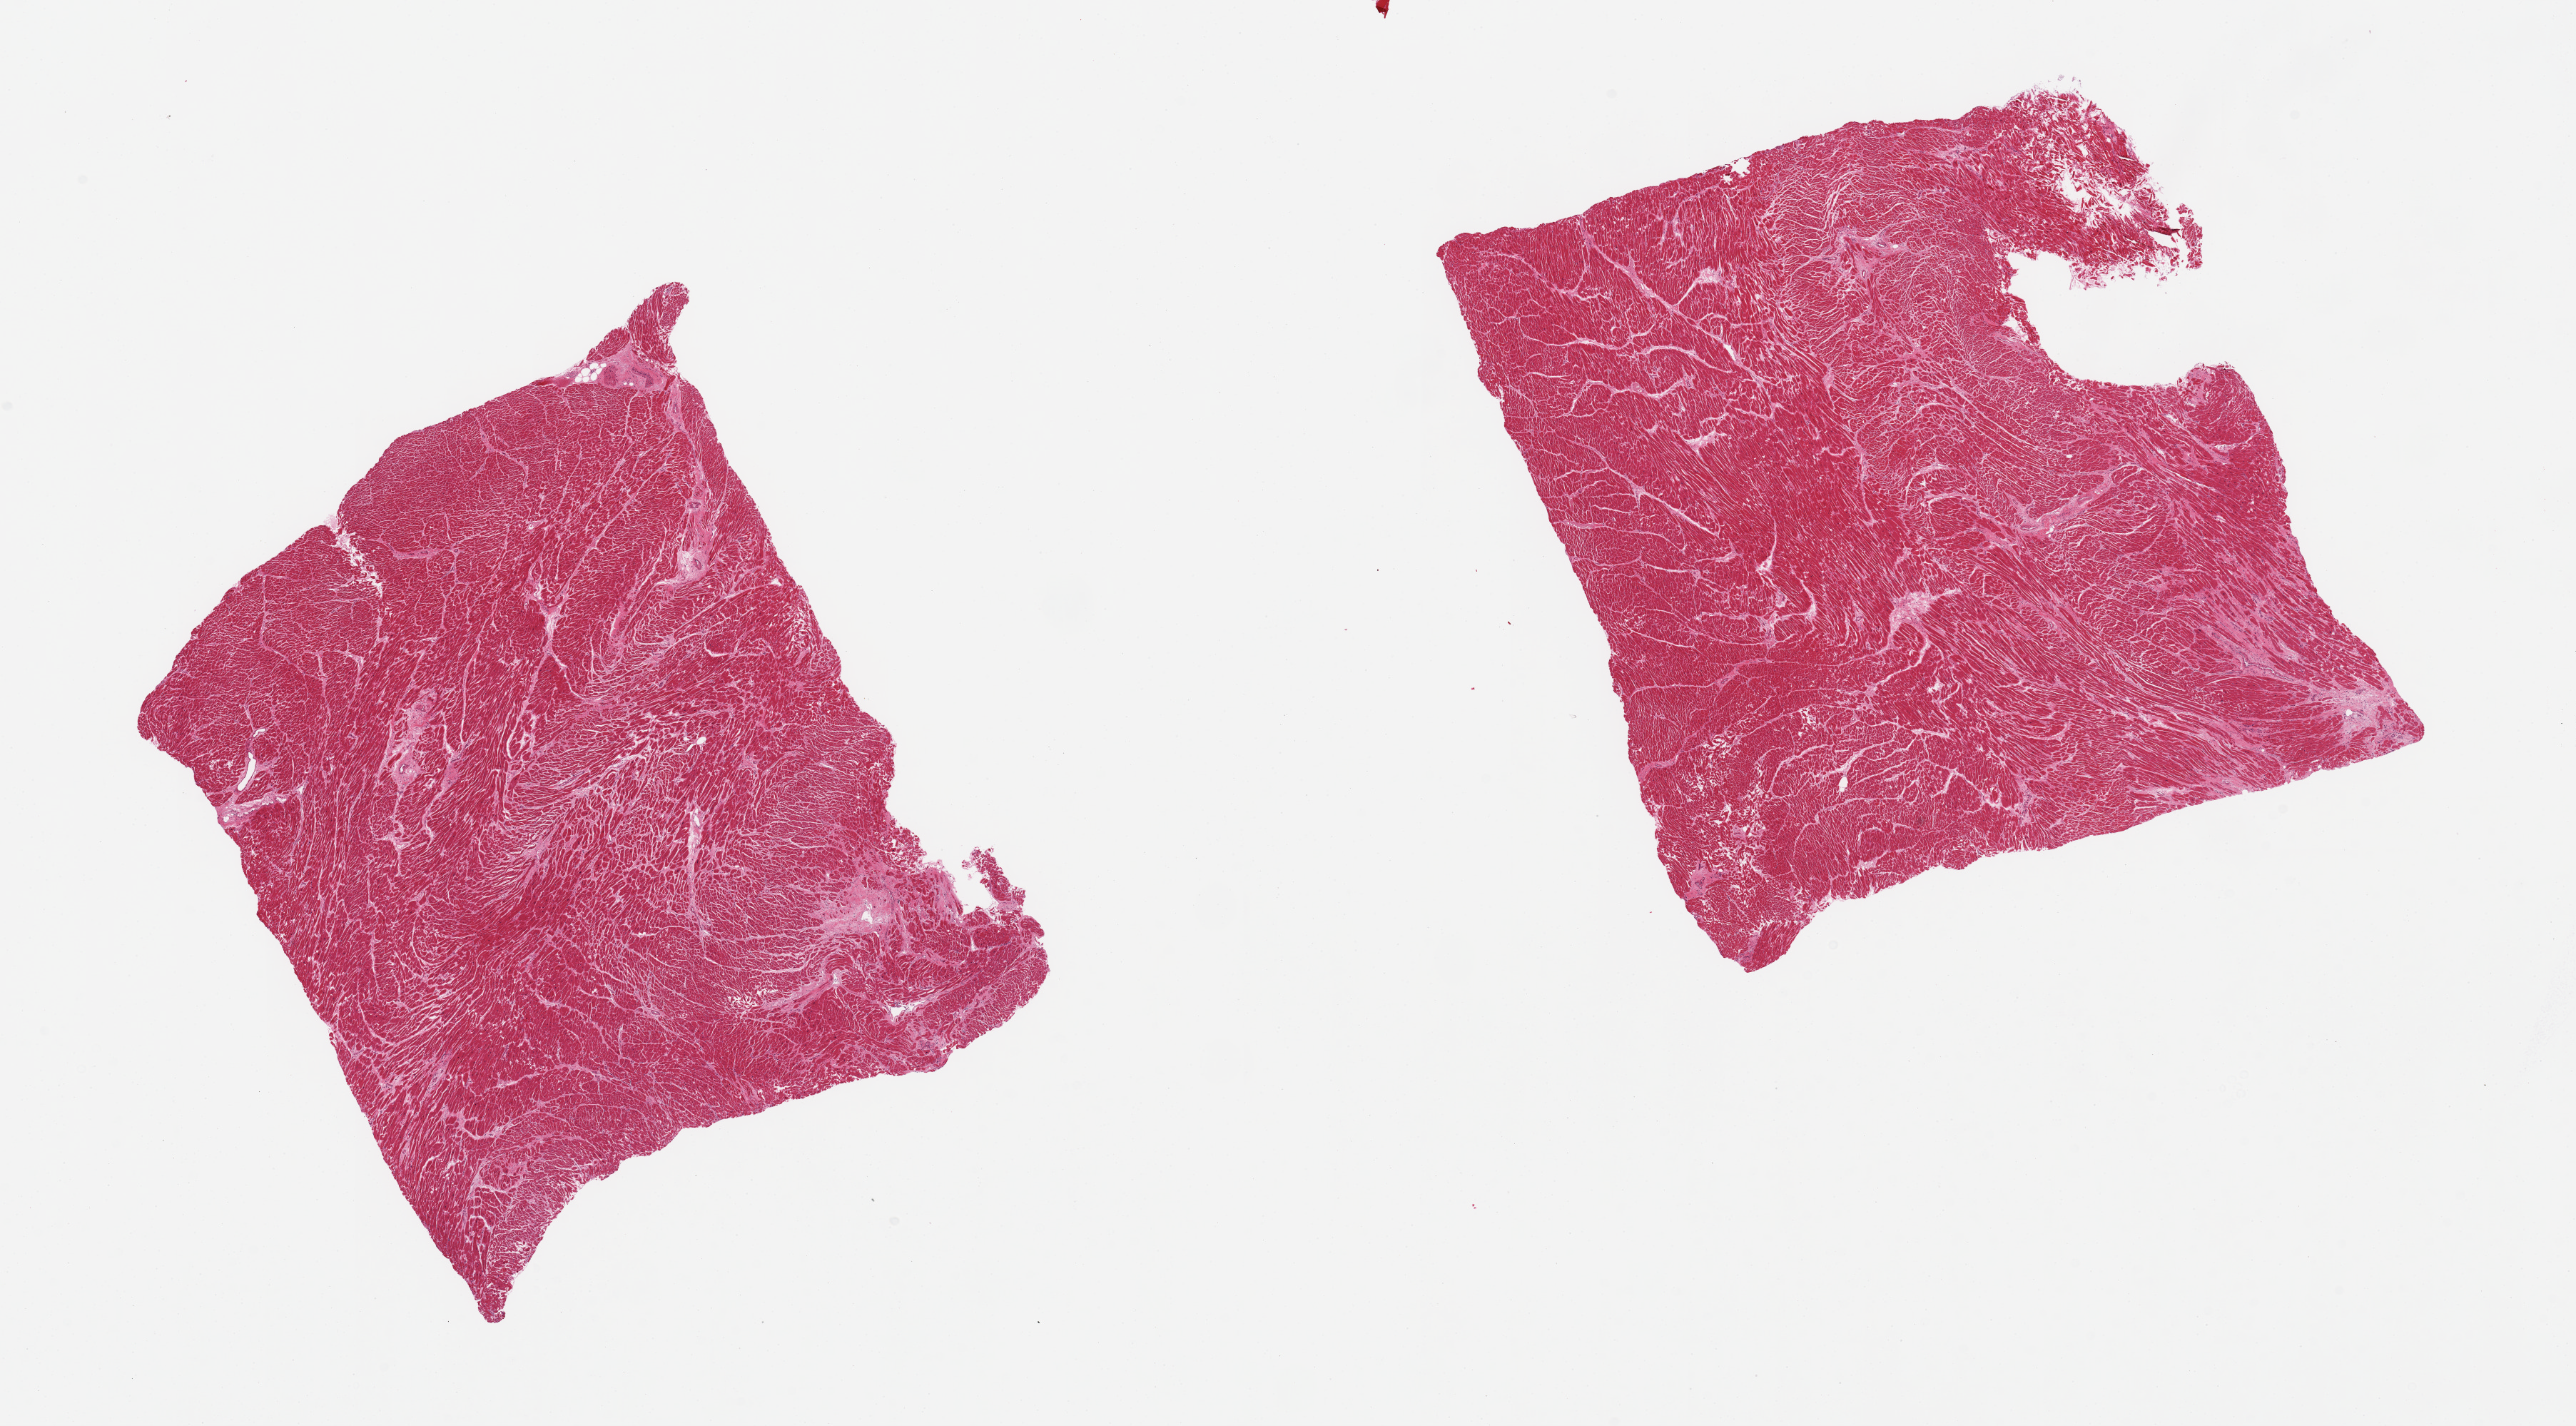
Haematoxylin and eosin whole-slide image, whole scanned area (about 28.5 x 15.8 mm, slide scanned at 20x) shown as a low-resolution overview, PAXgene-fixed paraffin-embedded (PFPE) section, sampled site (target tissue): heart, donor tissue sample. Male donor.
Reviewer comment on this tissue sample: 2 pieces, interstitial fibrosis.